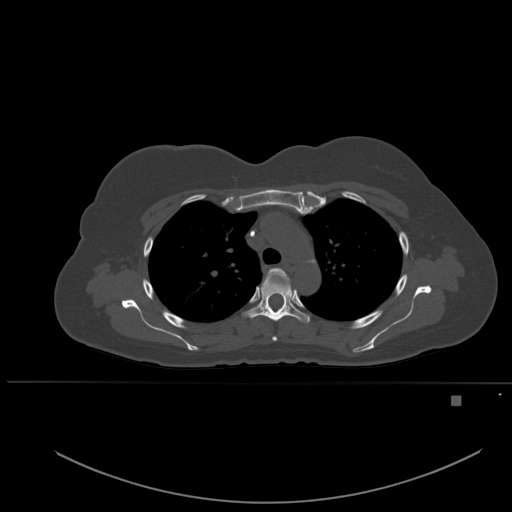
CT including the spine, one axial slice; slice 382 of 651 in the series (ordered by position); bone window (W 1800 / L 400 HU); 1.5 mm slice thickness; 512 × 512 image matrix. Female patient, age 49 years. Case-level facts recorded for this patient, not image findings: primary cancer: breast; vertebrae with lytic lesions (as recorded): L3, T12, L4.
Annotated regions visible in this slice (semi-automatically segmented with operator editing):
- T3 vertebra: bounding box (x1, y1, x2, y2) in pixels: (268, 268, 285, 341)
- T4 vertebra: (245, 272, 310, 322)